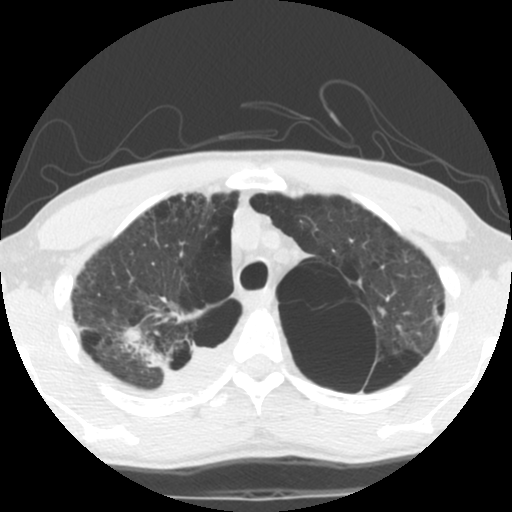
Low-dose screening chest CT, one axial slice. Slice 92 of 119 in the series (ordered by position). 140 kVp. Lung window (W 1500 / L -600 HU). 2.5 mm slice thickness. 512 × 512 image matrix, field of view 295 × 295 mm.
Outlined on this slice (expert manual segmentation):
- lesion 1 (tumor, upper lobe of right lung): bounding box <121,325,225,392> (left, top, right, bottom; pixels)